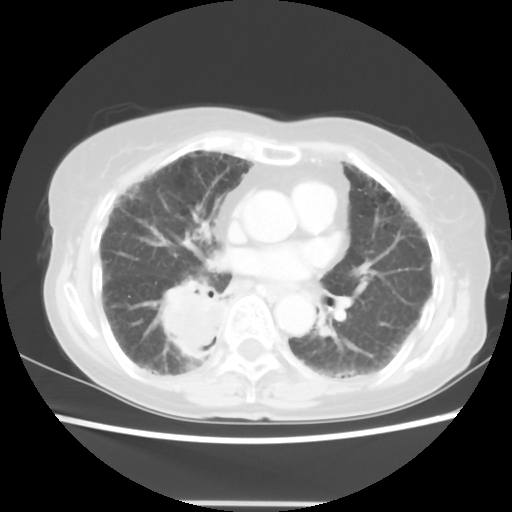
Chest CT, one axial slice; position 27 of 52 along the scan axis; 120 kVp; lung window (W 1500 / L -600 HU); 5 mm slice thickness; 512 × 512 image matrix, field of view 325 × 325 mm. Female patient, age 71 years. Case-level facts recorded for this patient, not image findings: clinical TNM (as recorded): T3 N0 M0.
Structures marked on this image (bounding box drawn by a radiologist):
- lung tumour (recorded histology: squamous cell carcinoma): bounding box [x1, y1, x2, y2] px = [154, 286, 232, 370]